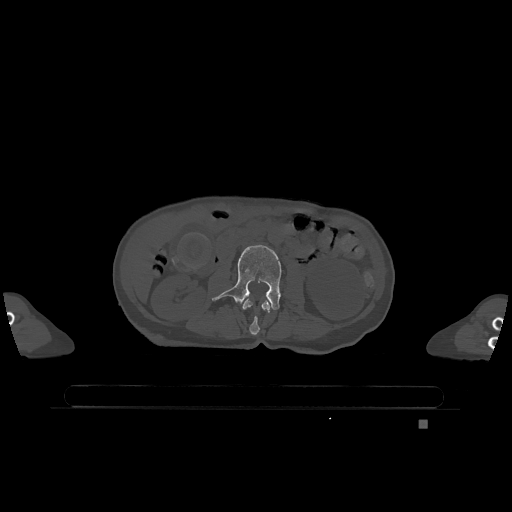
CT including the spine, one axial slice; slice 372 of 1317 in the series (ordered by position); bone window (W 1800 / L 400 HU); 0.5 mm slice thickness; 512 × 512 image matrix. Patient: female, 74 years. Case-level facts recorded for this patient, not image findings: primary cancer: lung.
Outlined on this slice (semi-automatically segmented with operator editing):
- L2 vertebra: box from (x=242, y=298) to (x=272, y=335) px
- L3 vertebra: (x=212, y=245)–(x=282, y=310)